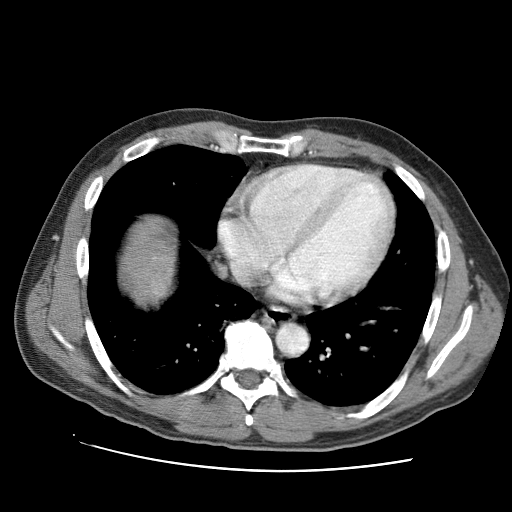
Contrast-enhanced abdominal CT (liver protocol), one axial slice; slice 91 of 95 in the series (ordered by position); reconstruction kernel STANDARD; 120 kVp; one of 2 acquisitions stored at this slice position; soft-tissue window (W 400 / L 40 HU); 2.5 mm slice thickness; 512 × 512 image matrix, field of view 360 × 360 mm. Case-level facts recorded for this patient, not image findings: diagnosis: hepatocellular carcinoma (patient treated with transarterial chemoembolisation; whether this scan precedes or follows treatment is not stated here); TNM stage (as recorded): Stage-IVA; Child-Pugh class: A; tumour differentiation: moderately differentiated; tumour nodularity: multinodular.
Structures marked on this image (semi-automatic segmentation, software-assisted and operator-edited):
- liver parenchyma outside the tumour (the mass and vessels are separate outlines, so this box may not span the whole liver): box from (x=120, y=214) to (x=176, y=299) px